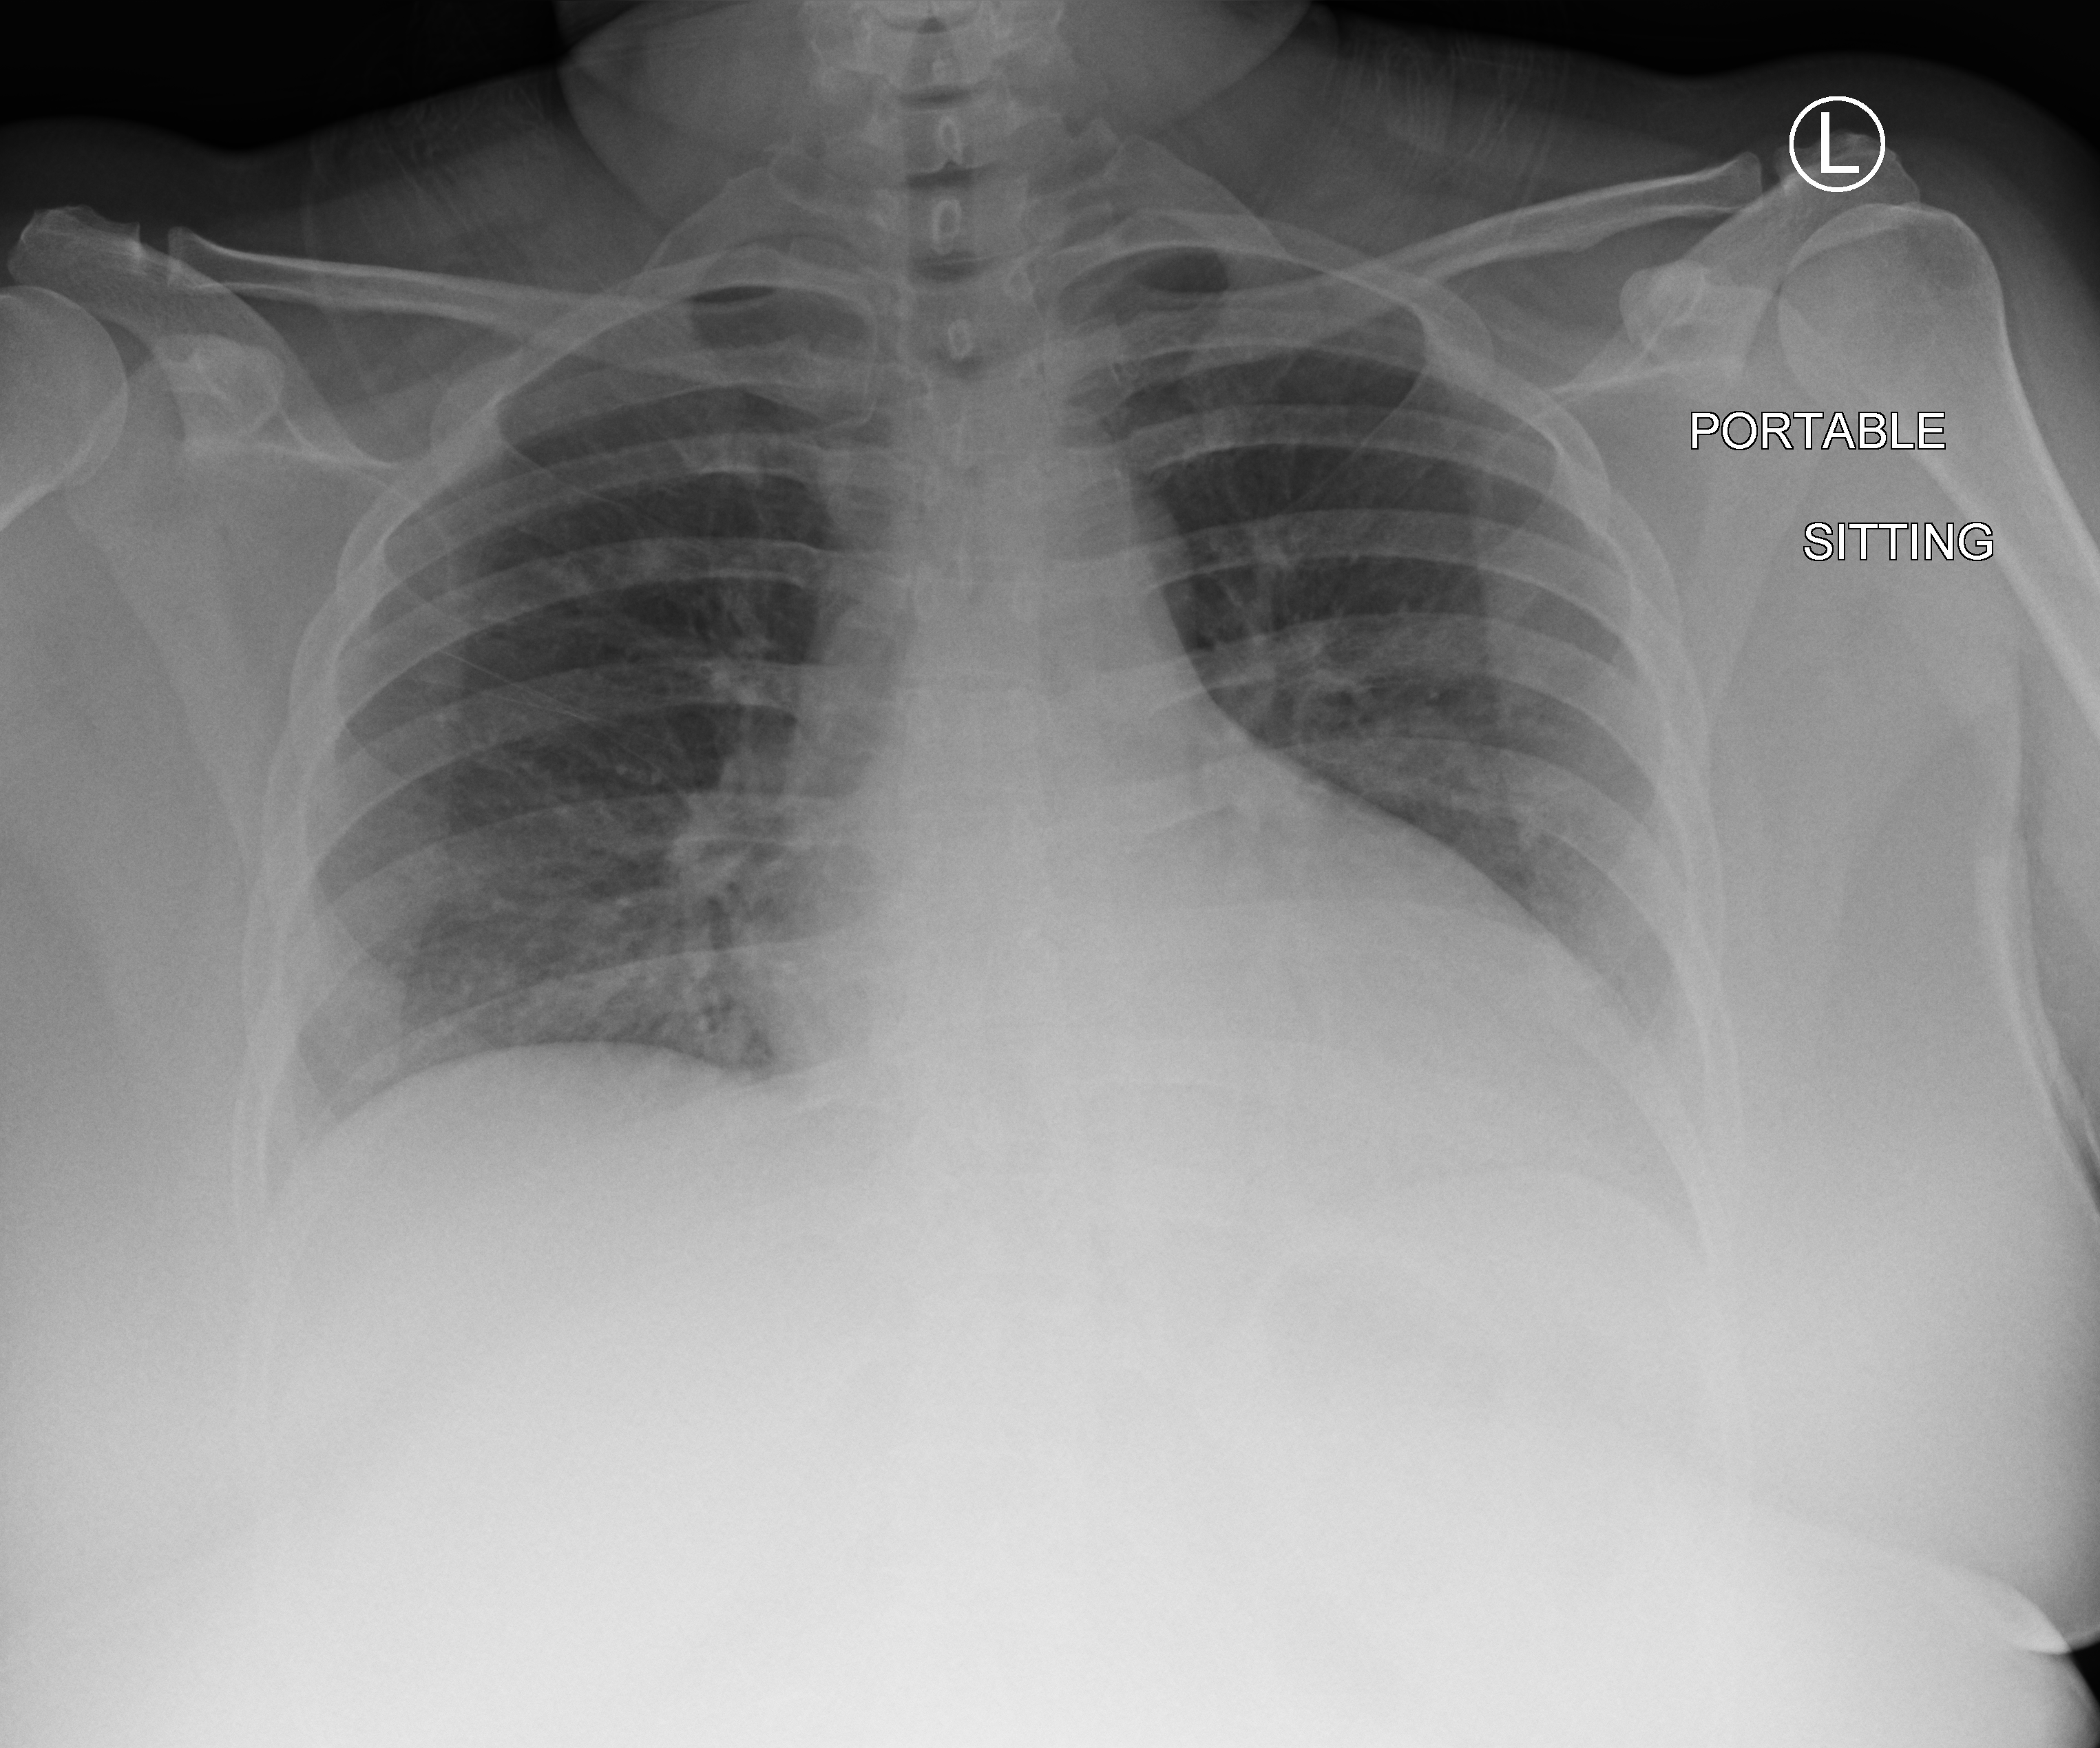
Chest X-ray (portable), anteroposterior (AP) projection. Patient hospitalised with COVID-19; female, aged 18–59 years.
Admission-level facts for this patient (not findings on this image; timing relative to this image not recorded): length of hospital stay: 1 day; admitted to intensive care during this hospital stay: no; mechanically ventilated during this hospital stay: no.